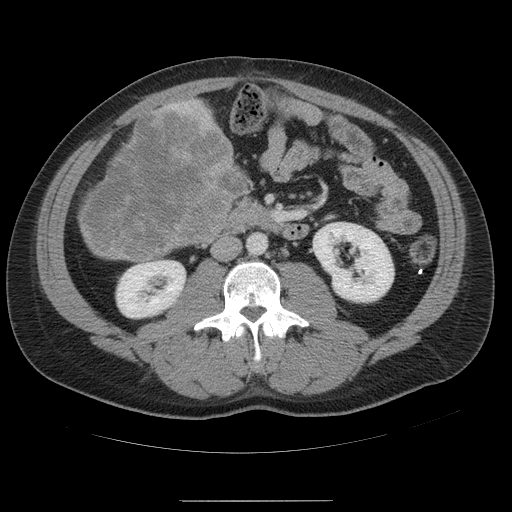
Contrast-enhanced abdominal CT, one axial slice. Slice 14 of 54 in the series (ordered by position). Intravenous contrast given. Soft-tissue window (W 400 / L 40 HU). 5 mm slice thickness. 512 × 512 image matrix, field of view 436 × 436 mm. Male patient, age 40 years. Case-level facts recorded for this patient, not image findings: diagnosis: colorectal cancer liver metastases, imaged before liver resection; multiple liver metastases: no; largest metastasis: 15 cm; disease in both lobes: no.
Outlined on this slice (expert manual segmentation):
- liver: box from (x=79, y=99) to (x=248, y=263) px
- liver metastasis: (x=81, y=110)–(x=249, y=261)